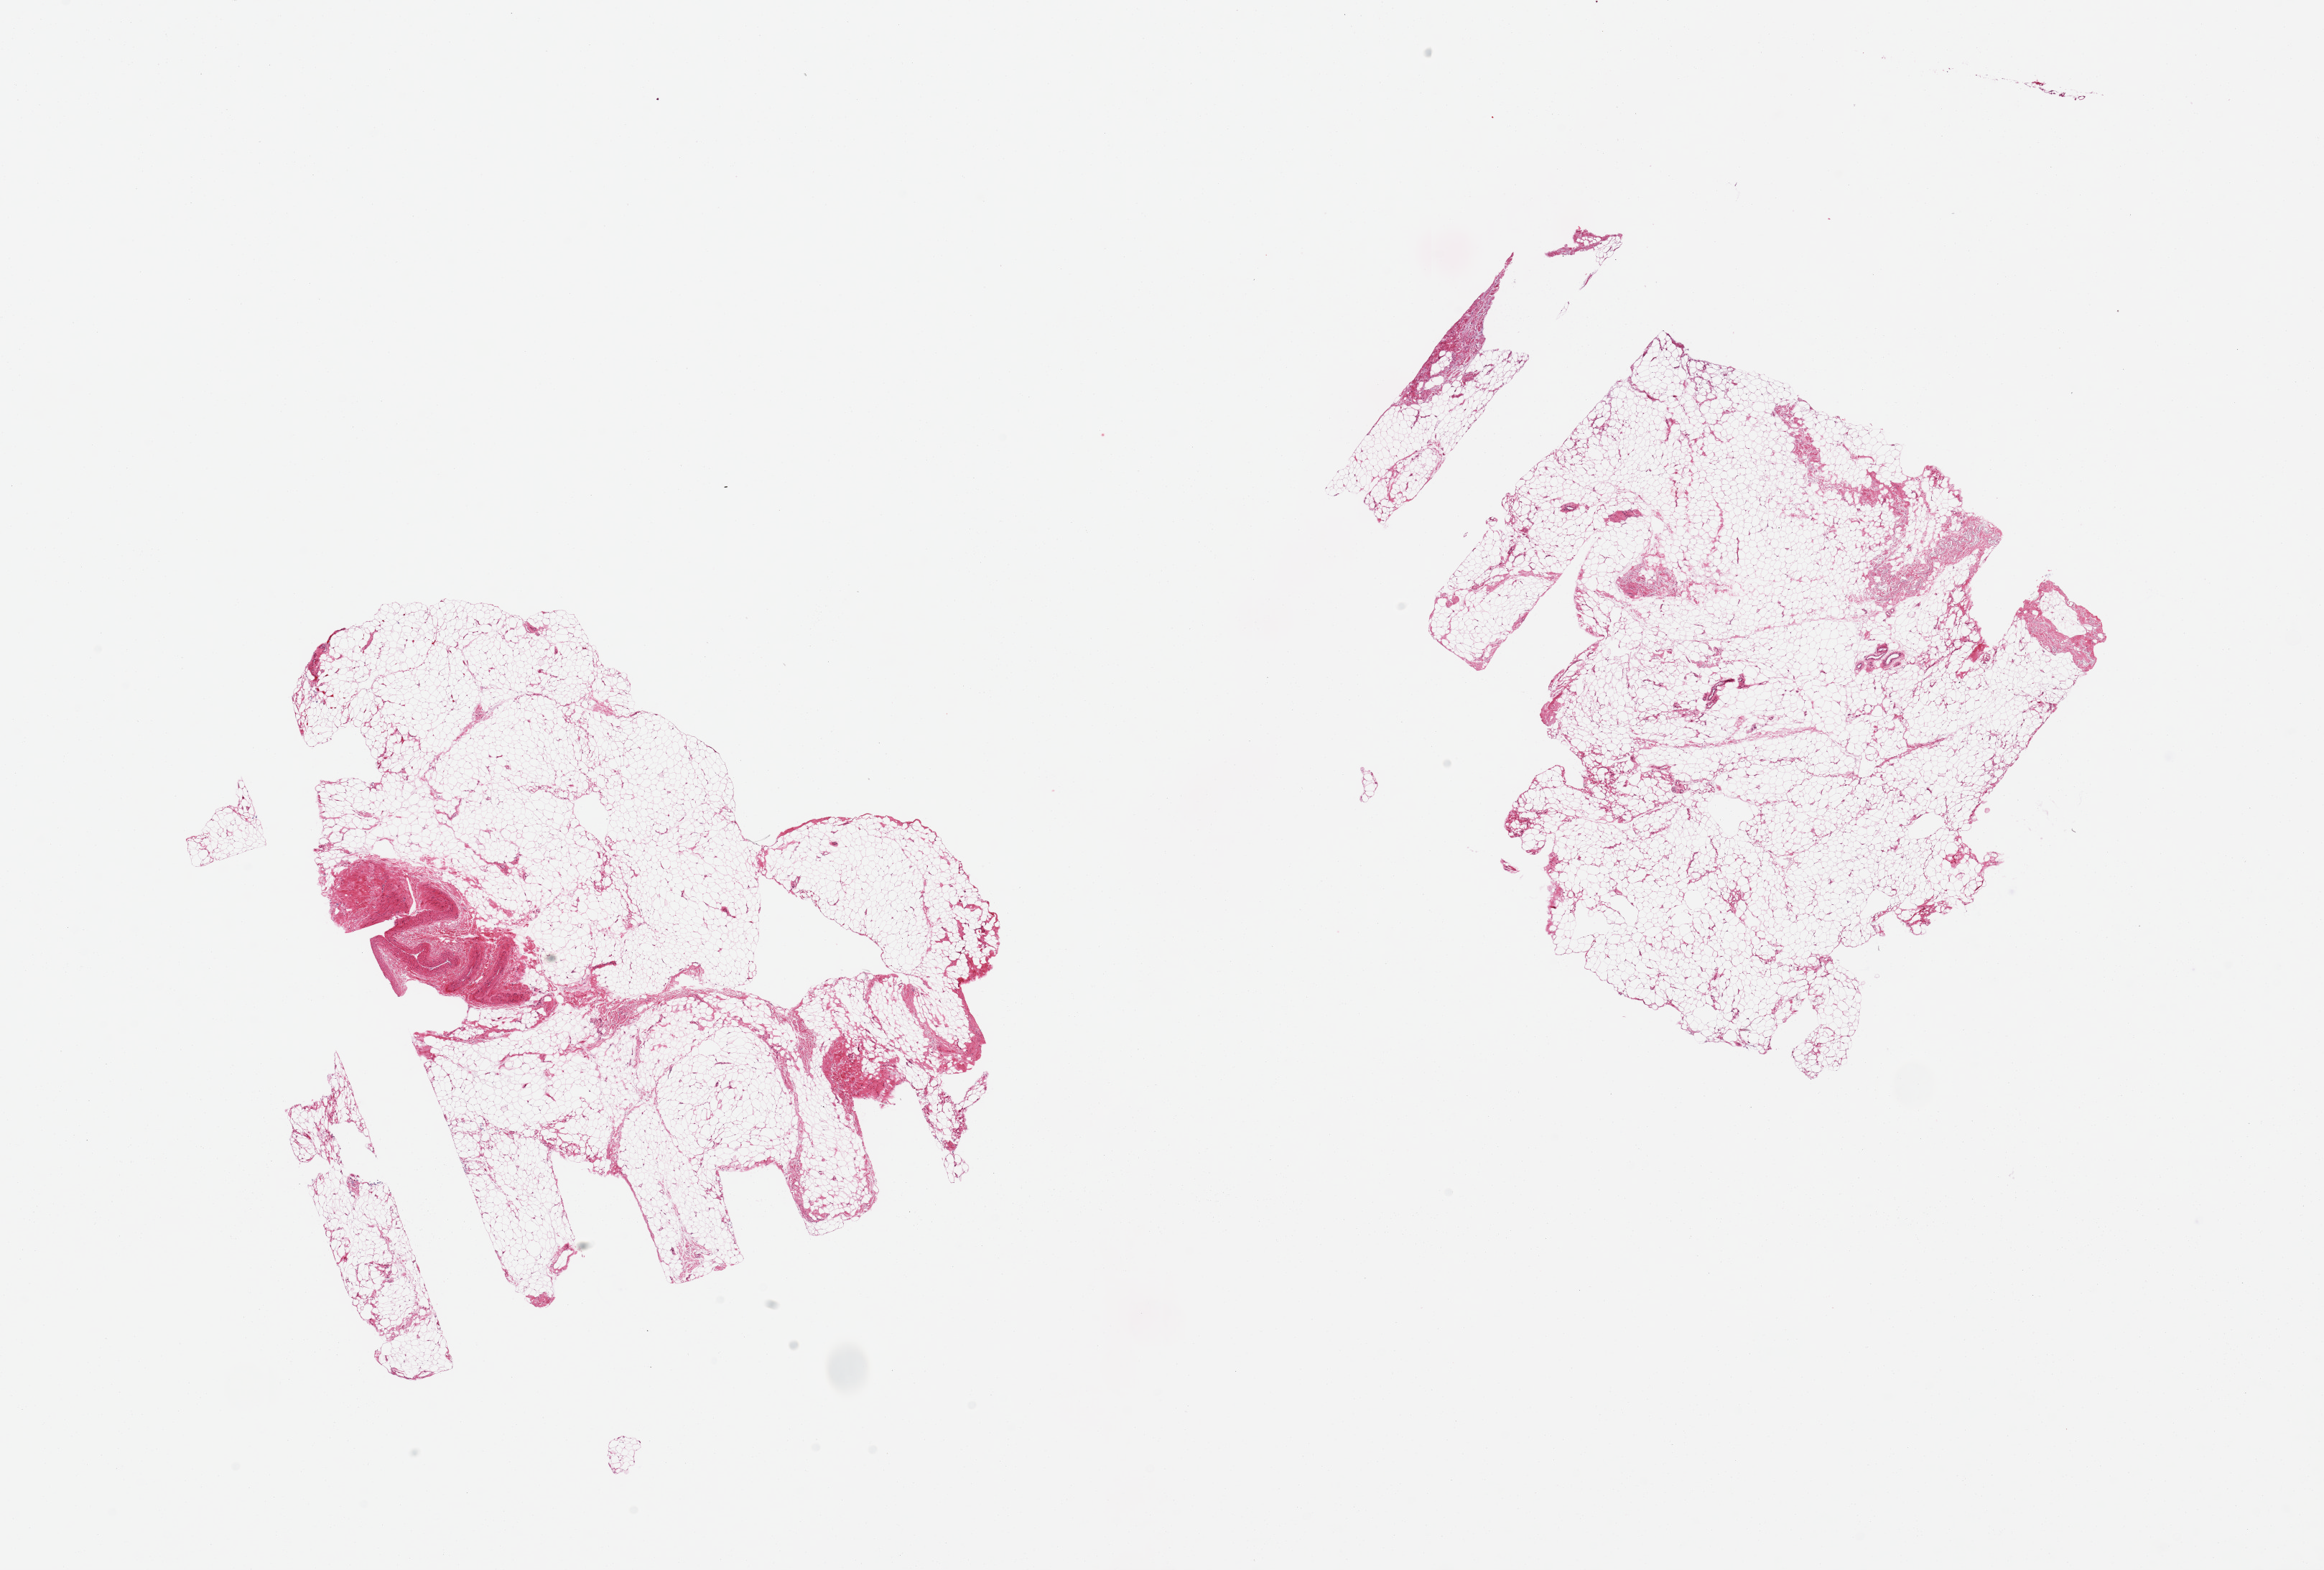
Haematoxylin and eosin whole-slide image, low-resolution overview of the scanned area, about 25.6 x 17.3 mm. PAXgene-fixed, paraffin-embedded tissue. Target tissue: adipose tissue. Tissue donor sample.
- review note (as recorded): 2 pieces; mature adipose tissue with fibrovascular component and larger vessel